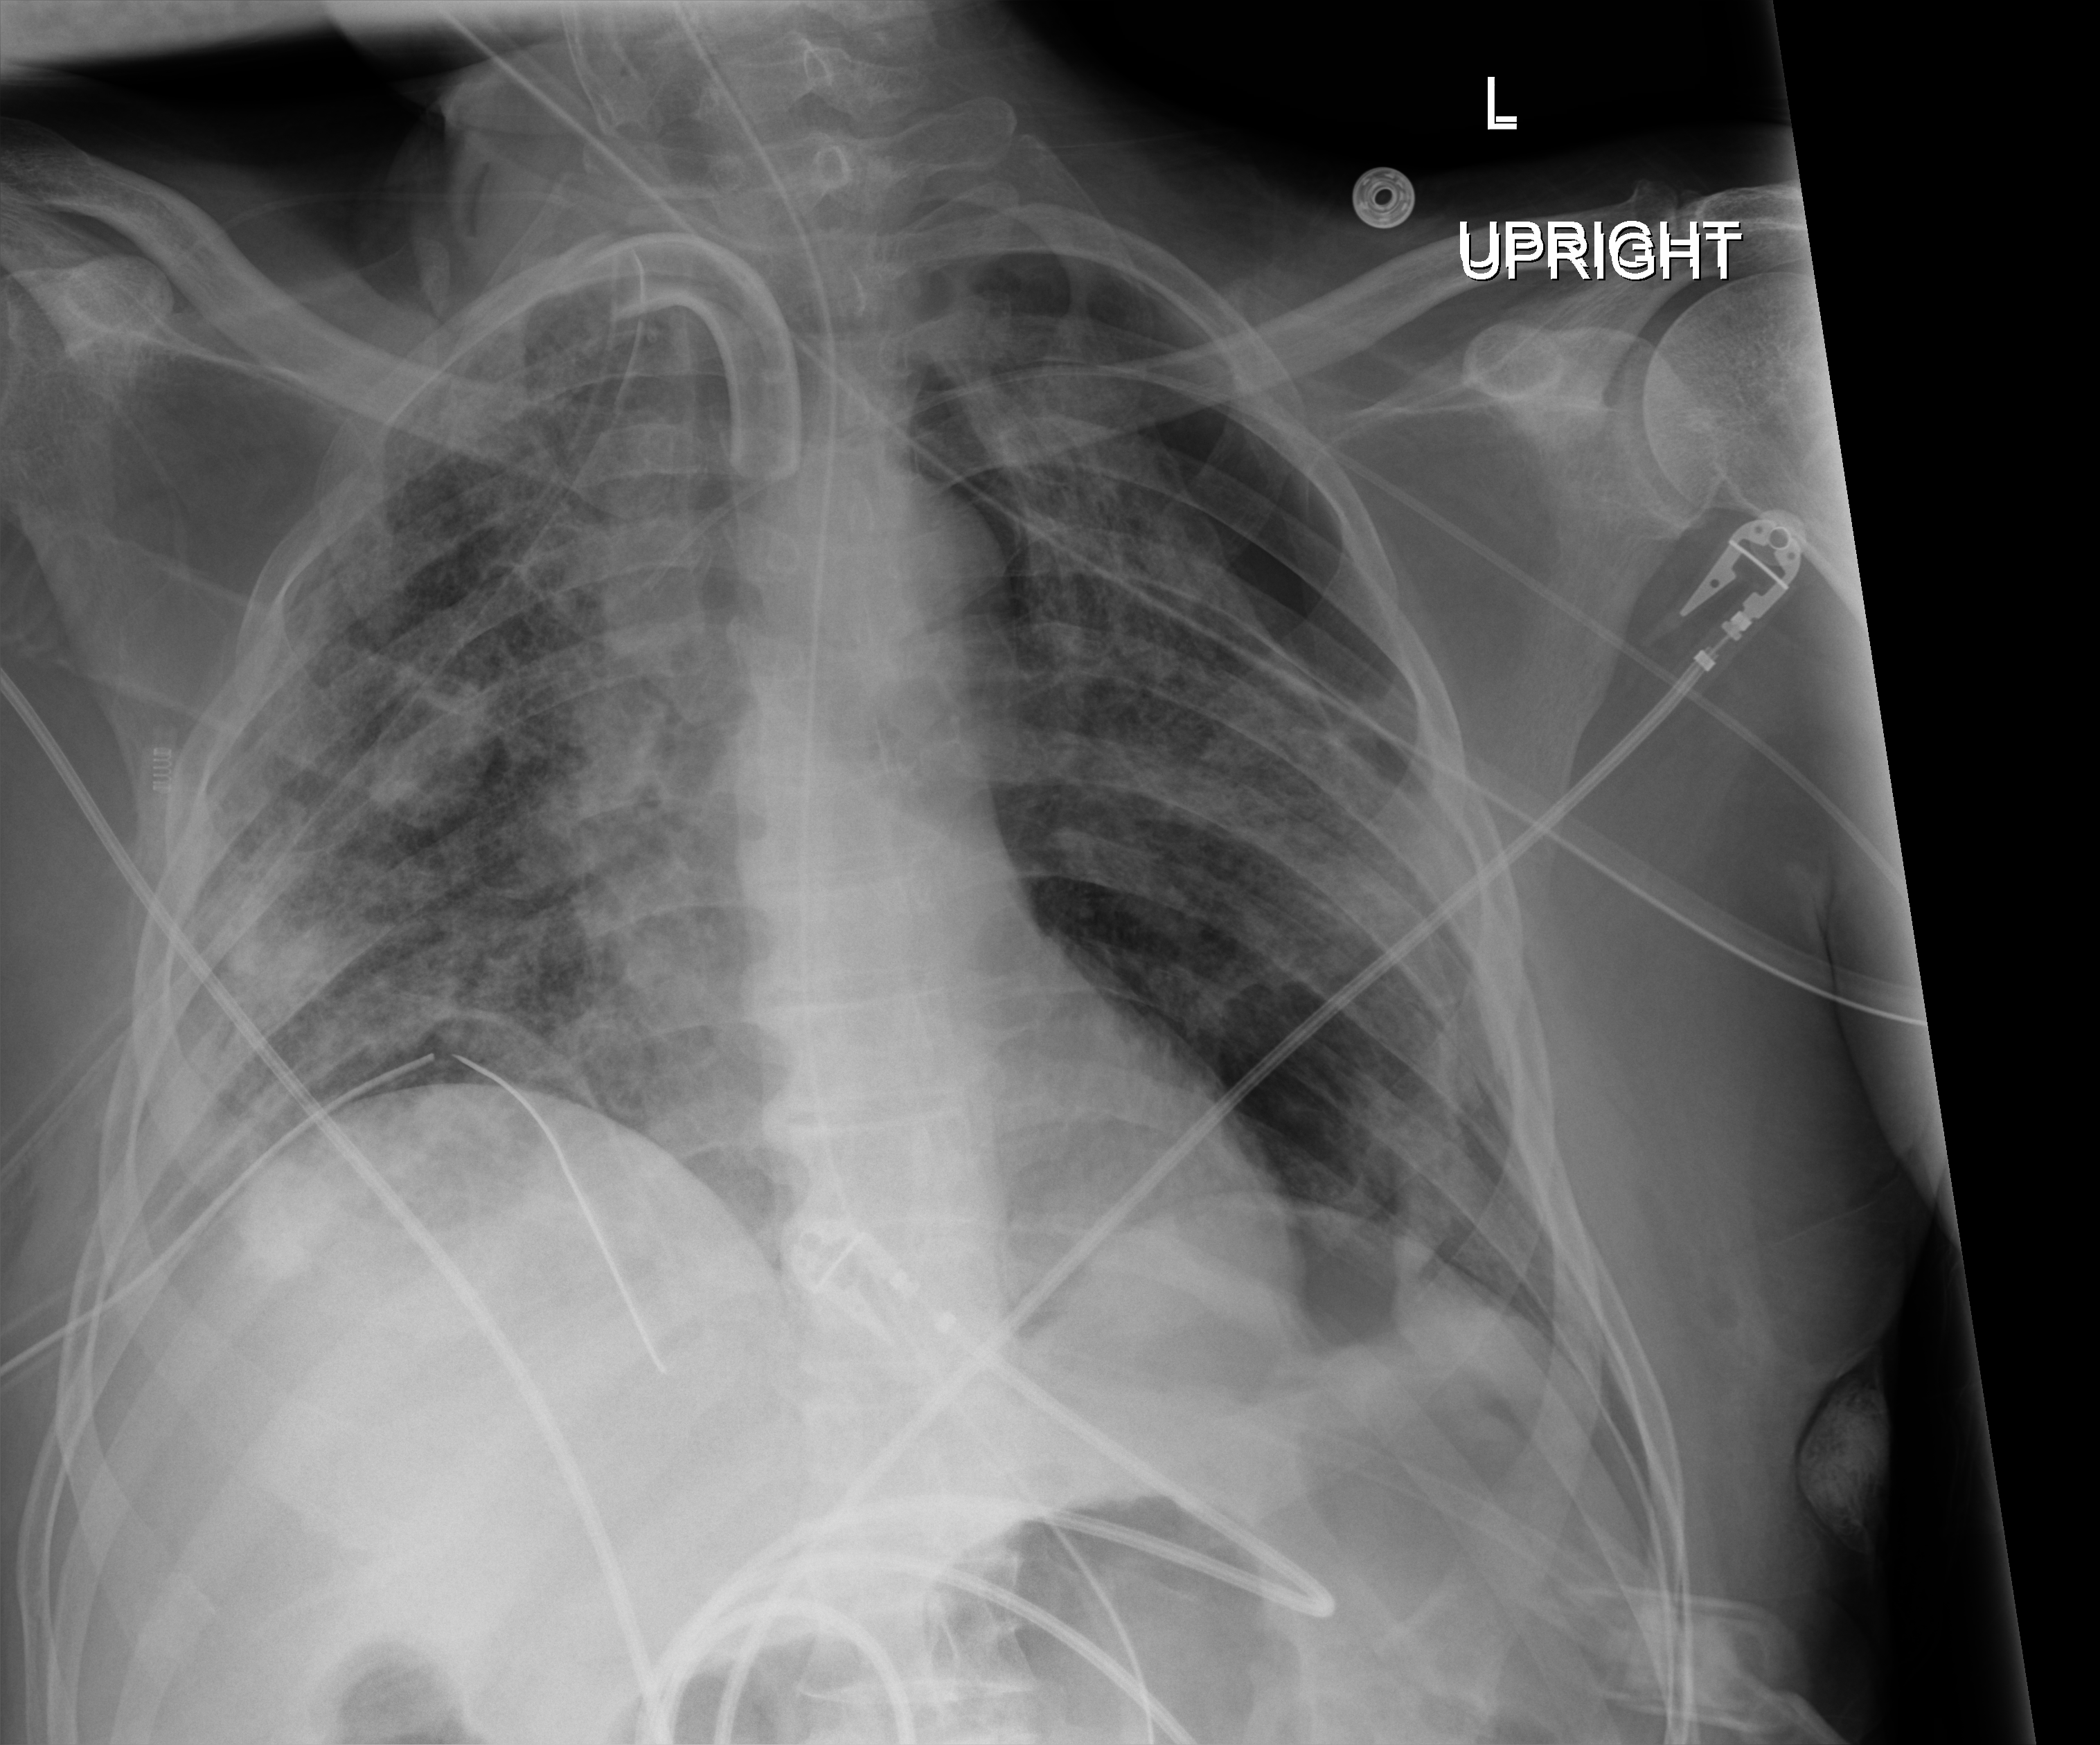
Portable chest radiograph. Patient hospitalised with COVID-19; male, aged 18–59 years.
Hospital-stay facts (about this admission, not read from this image; timing relative to this image not recorded): admitted to intensive care during this hospital stay: yes.